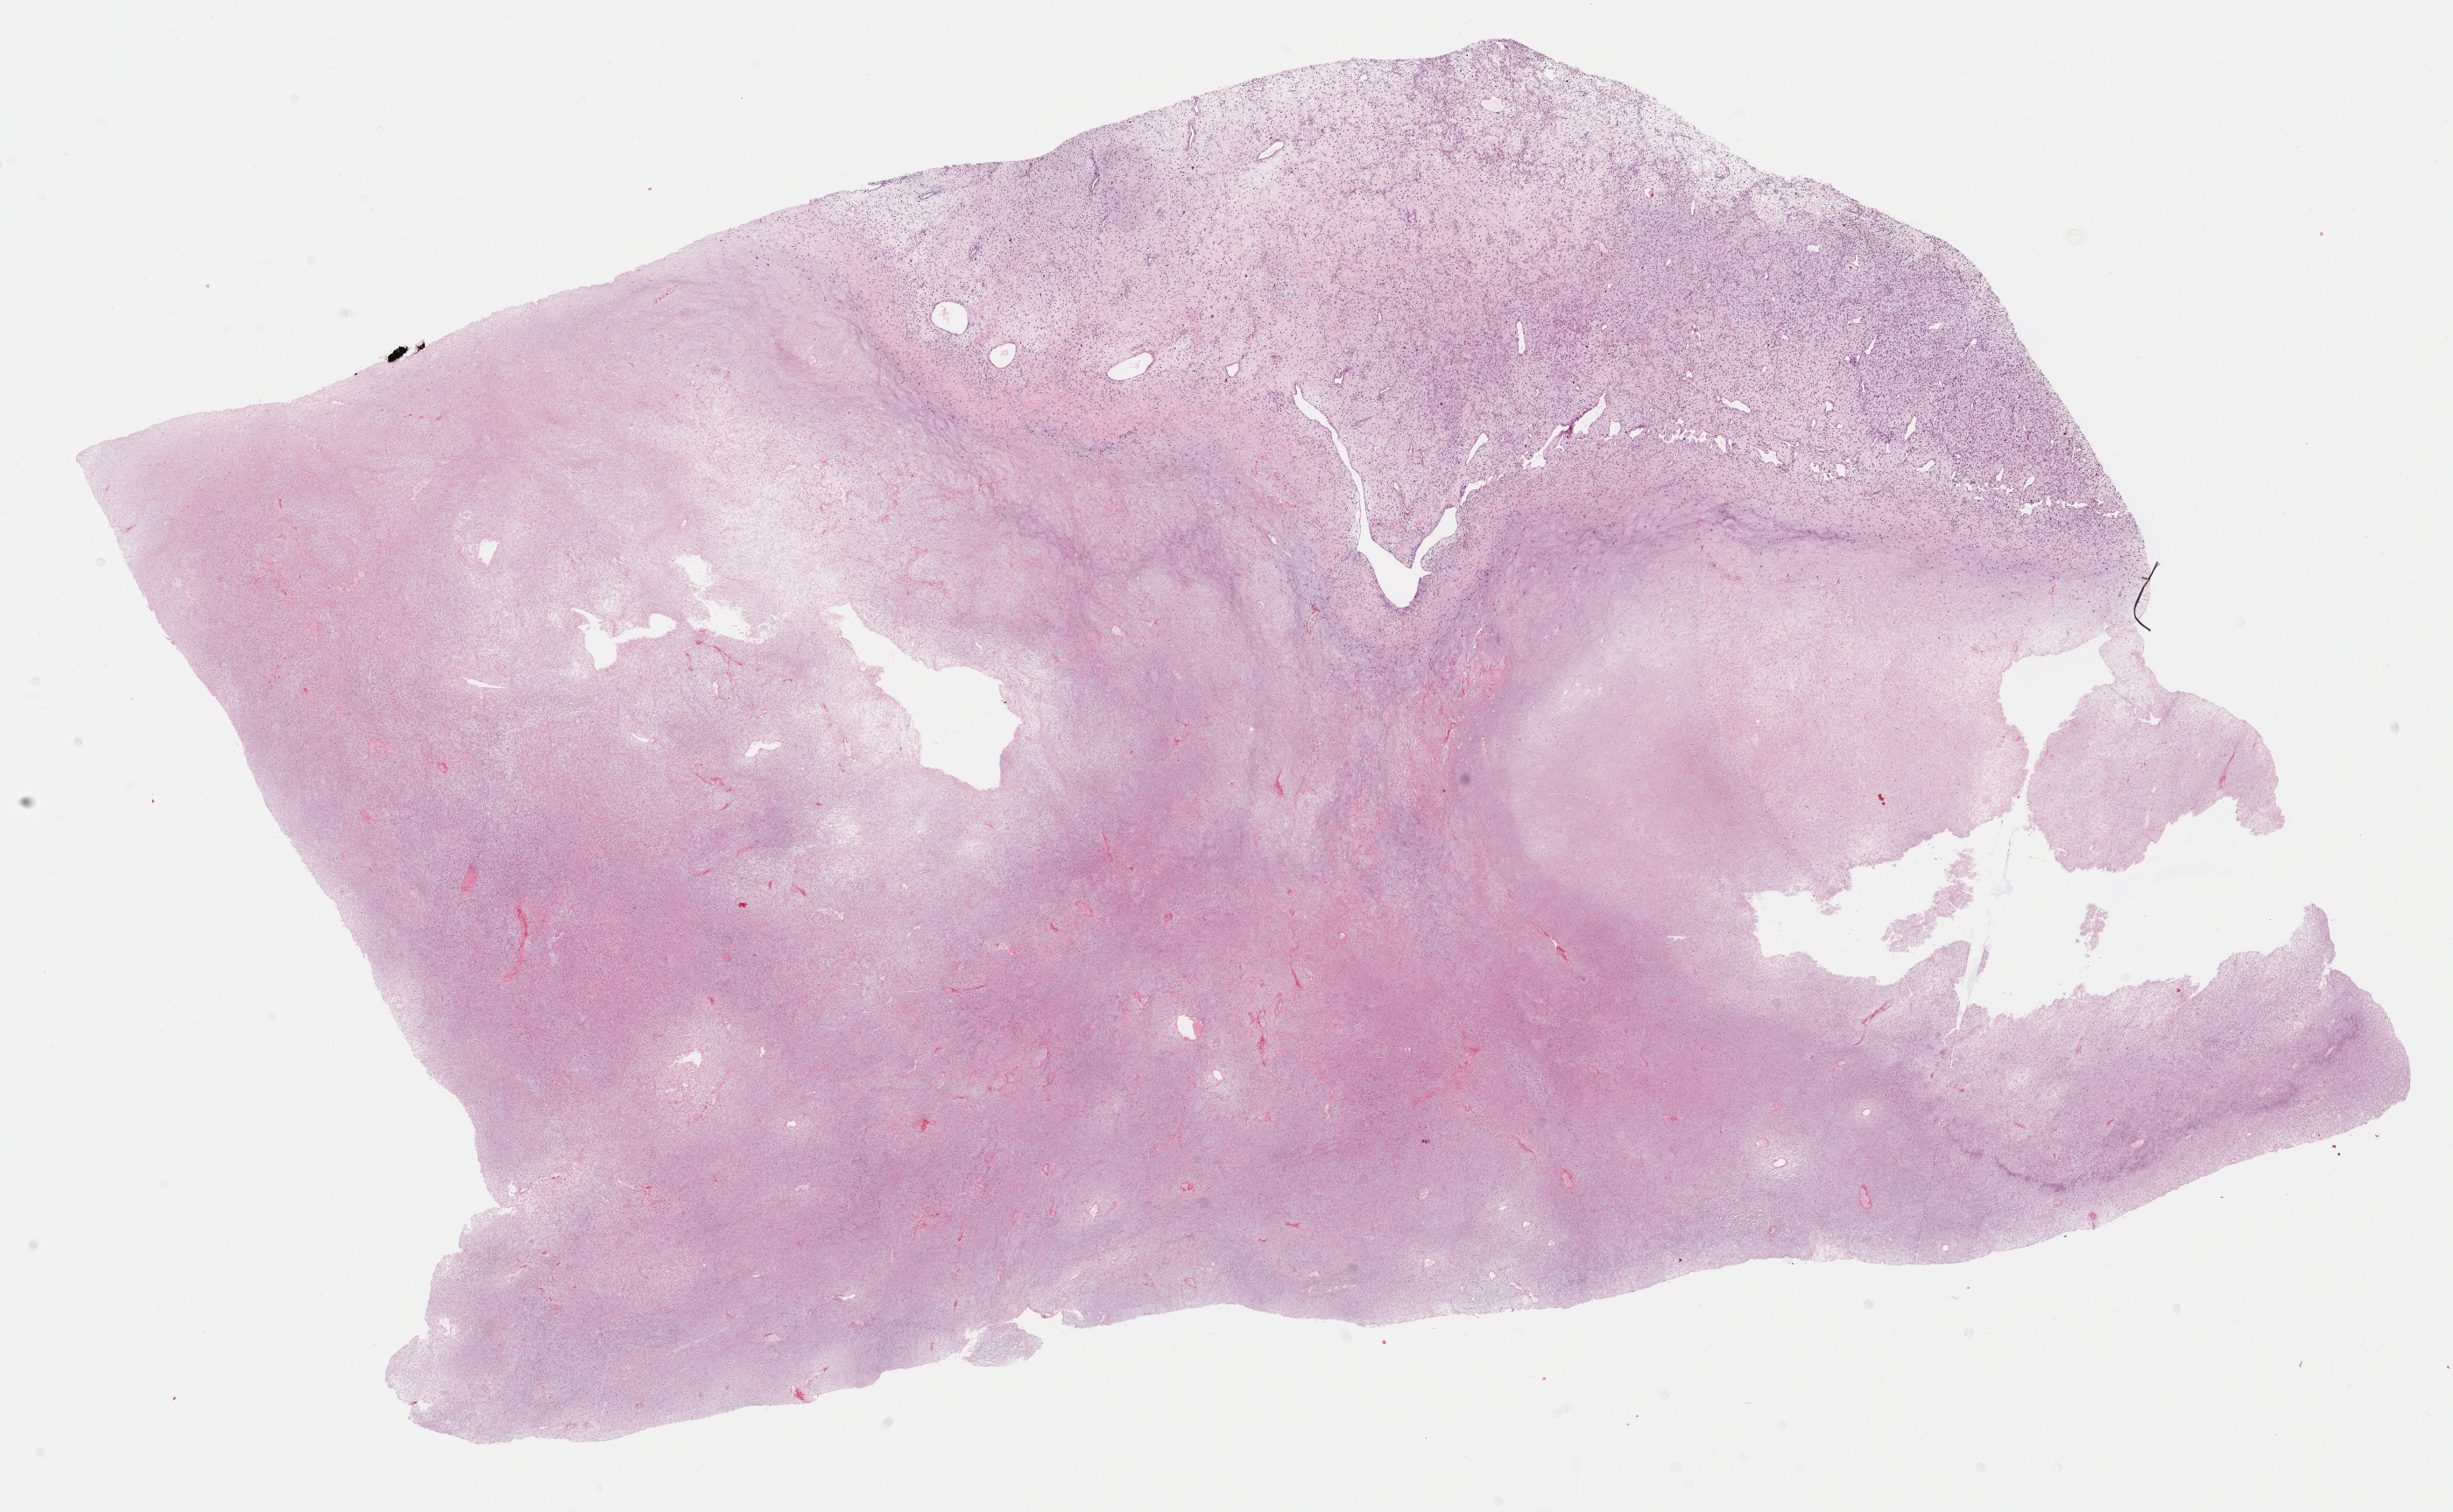
Whole-slide histology image, H&E-stained — whole scanned area (about 22.7 x 14.0 mm, acquisition: 40x scan) shown as a low-resolution overview; formalin-fixed paraffin-embedded (FFPE) diagnostic section; primary tumour sample from the retroperitoneum and peritoneum. Patient: male, age at initial diagnosis 57 years.
Diagnosis: Fibromyxosarcoma (retroperitoneum).